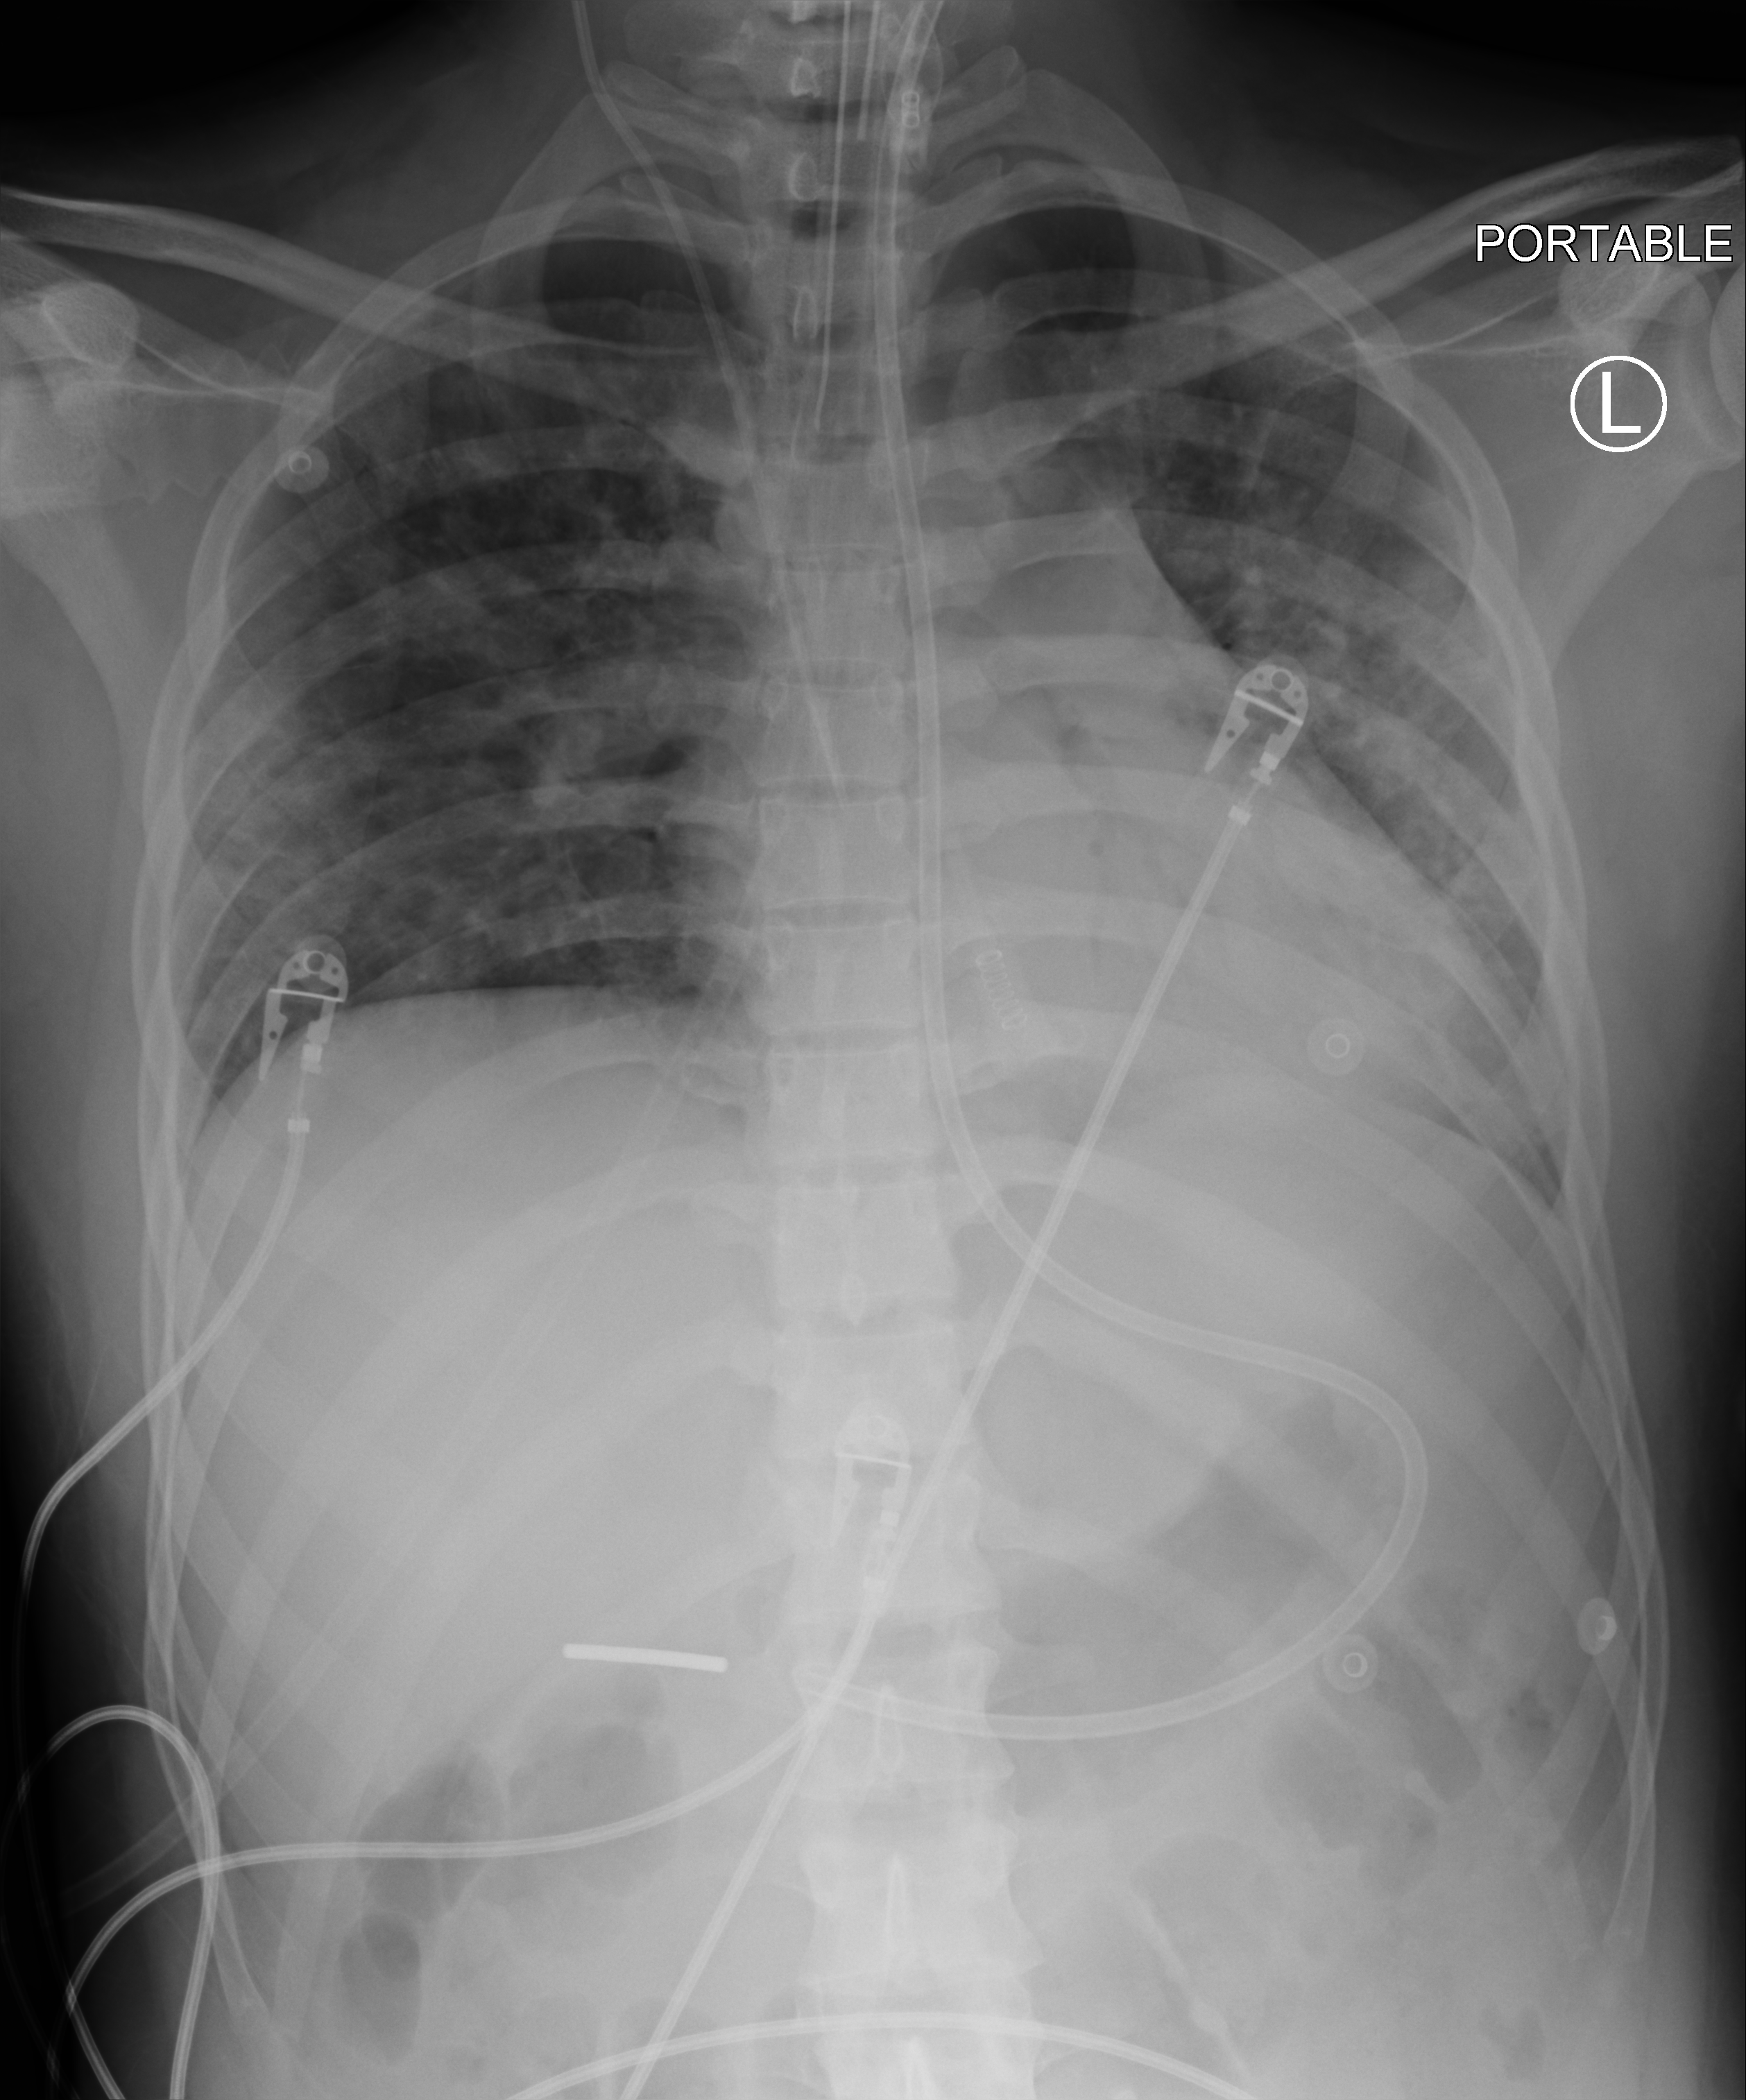
Bedside chest radiograph (computed radiography); anteroposterior (AP) projection. Male patient hospitalised with COVID-19, age 18–59 years.
From the hospital-stay record, not from the radiograph (when in the stay this image was taken is not recorded):
- admitted to intensive care during this hospital stay: no
- length of hospital stay: 23 days
- COPD (admission record): no